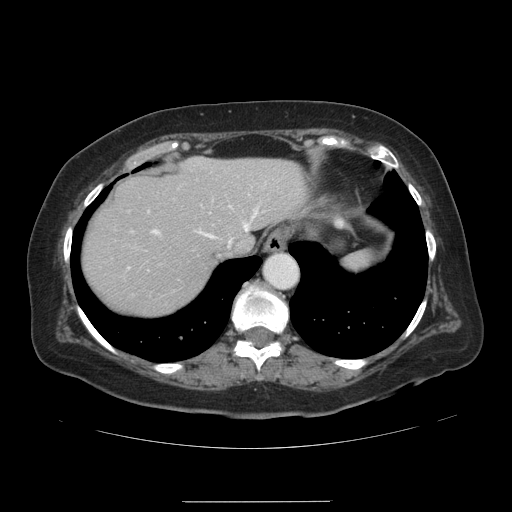
Contrast-enhanced abdominal CT, one axial slice. Position 112 of 141 along the scan axis. 120 kVp. Intravenous contrast given. Soft-tissue window (W 400 / L 40 HU). 512 × 512 image matrix. Female patient, age 74 years. Case-level facts recorded for this patient, not image findings: diagnosis: colorectal cancer liver metastases, imaged before liver resection; multiple liver metastases: yes; largest metastasis: 7 cm; disease in both lobes: yes.
Annotated regions visible in this slice (manually delineated by an expert):
- hepatic veins: bounding box [x1, y1, x2, y2] px = [201, 206, 259, 248]
- liver: [83, 158, 306, 314]
- planned liver remnant (the part of the liver to remain after resection): [83, 158, 306, 314]
- portal vein (with intrahepatic branches): [128, 229, 159, 268]